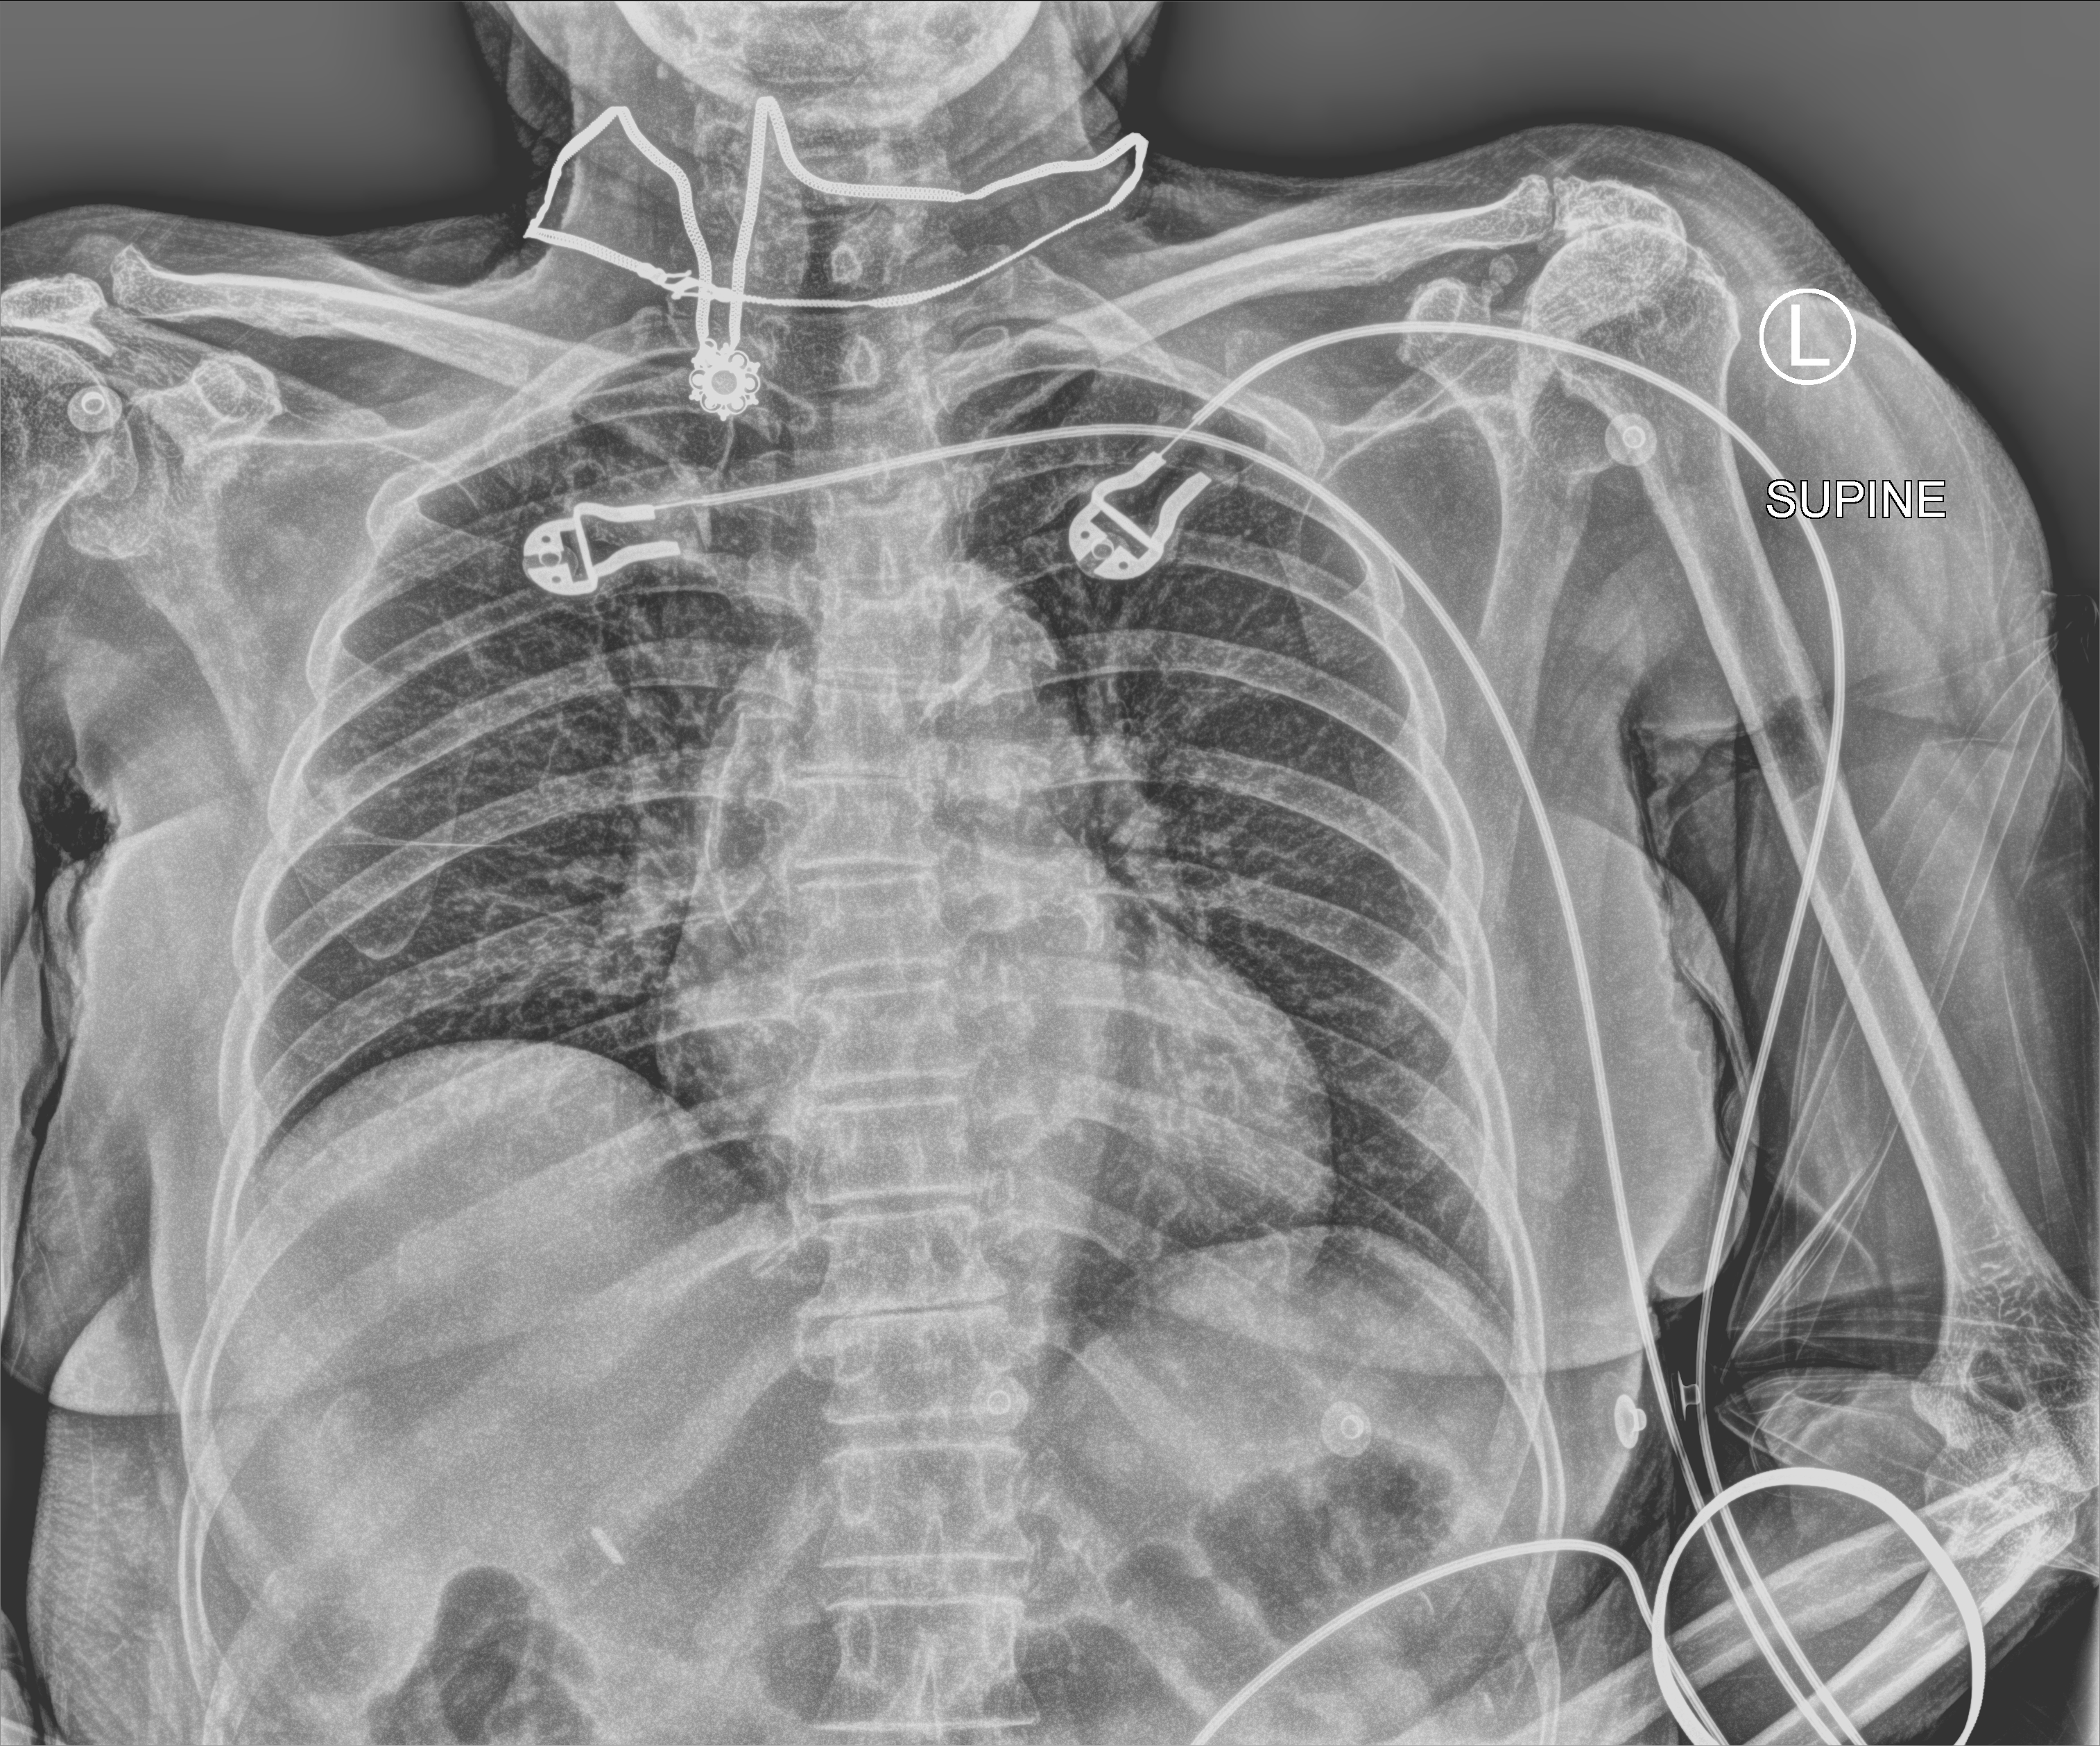
Bedside chest radiograph (computed radiography), anteroposterior (AP) projection. Patient hospitalised with COVID-19; female, aged 75–90 years.
Hospital-stay facts (about this admission, not read from this image; timing relative to this image not recorded): admitted to intensive care during this hospital stay: no; mechanically ventilated during this hospital stay: no.